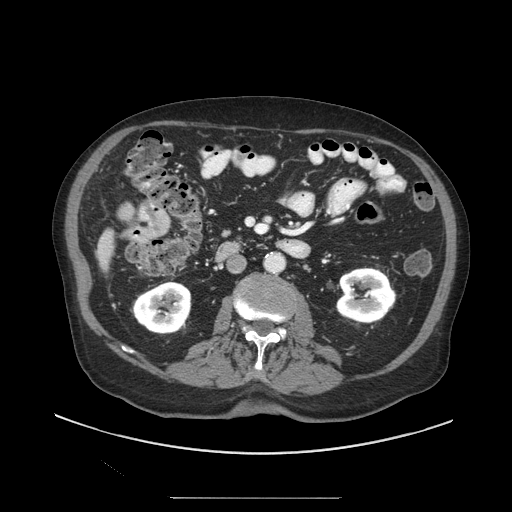
Contrast-enhanced abdominal CT (liver protocol), one axial slice. Slice 29 of 97 in the series (ordered by position). Reconstruction kernel STANDARD. 140 kVp. Soft-tissue window (W 400 / L 40 HU). 2.5 mm slice thickness. 512 × 512 image matrix, field of view 450 × 450 mm. From the clinical record (not read from this slice): diagnosis: hepatocellular carcinoma (patient treated with transarterial chemoembolisation; whether this scan precedes or follows treatment is not stated here); TNM stage (as recorded): Stage-IIIC; Child-Pugh class: A; tumour differentiation: well differentiated; tumour nodularity: uninodular.
Outlined on this slice (semi-automatic segmentation, software-assisted and operator-edited):
- liver parenchyma outside the tumour (the mass and vessels are separate outlines, so this box may not span the whole liver): bounding box [x1, y1, x2, y2] px = [96, 228, 114, 270]